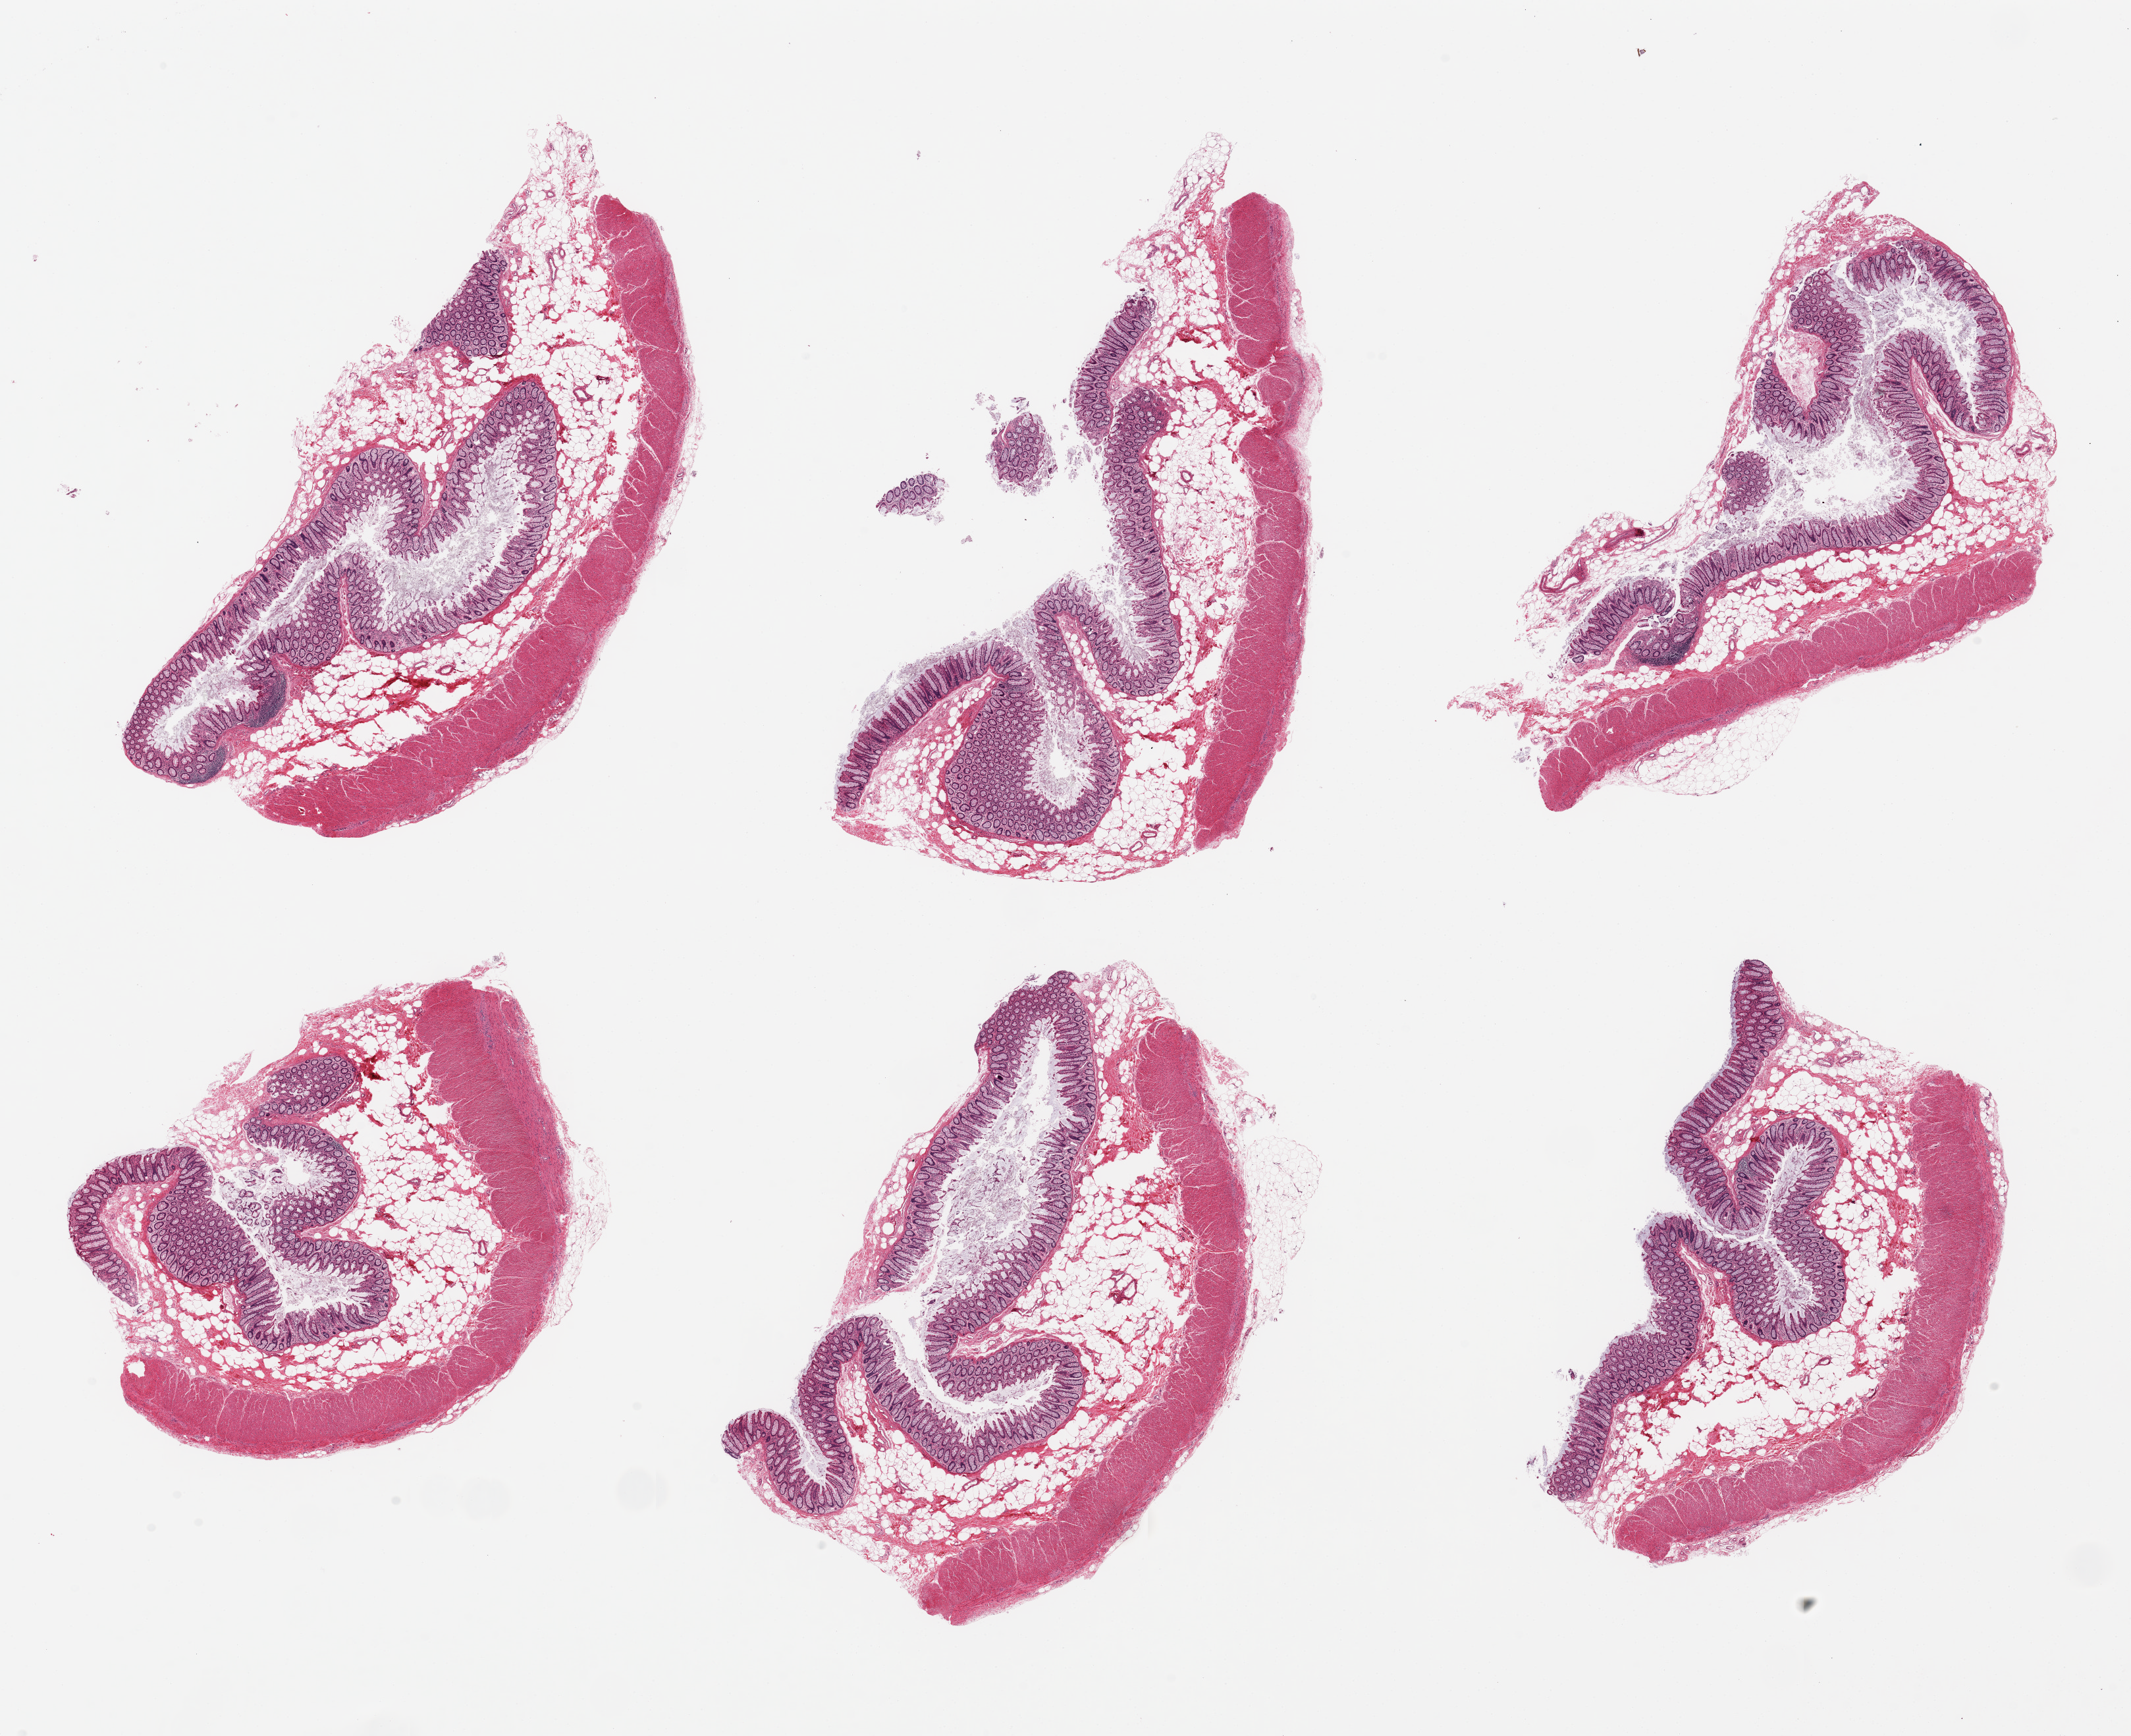
Whole-slide image, hematoxylin and eosin (H&E) stain — shown as a low-resolution overview of the whole scanned area (about 25.6 x 20.8 mm). PAXgene-fixed, paraffin-embedded tissue. Sampled site (target tissue): transverse colon. Tissue donor sample. Male donor.
Review note (as recorded): 6 pieces ~8x3mm. Mucosa remarkably well-preserved, ~10-20% of thickness.